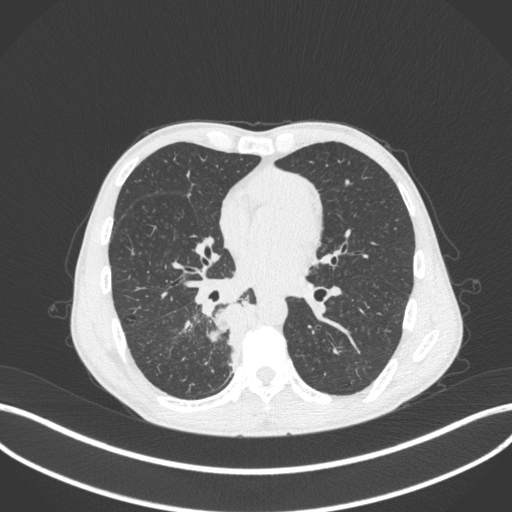
Chest CT, one axial slice; slice 179 of 371 in the series (ordered by position); reconstruction kernel B31f; 120 kVp; lung window (W 1500 / L -600 HU); 512 × 512 image matrix, field of view 400 × 400 mm. Patient: male, 58 years. Case-level facts recorded for this patient, not image findings: clinical TNM (as recorded): T3 N1 M1.
Outlined on this slice (rectangle marked by the reading radiologist):
- lung tumour (recorded histology: squamous cell carcinoma): bounding box [x1, y1, x2, y2] px = [201, 297, 257, 370]